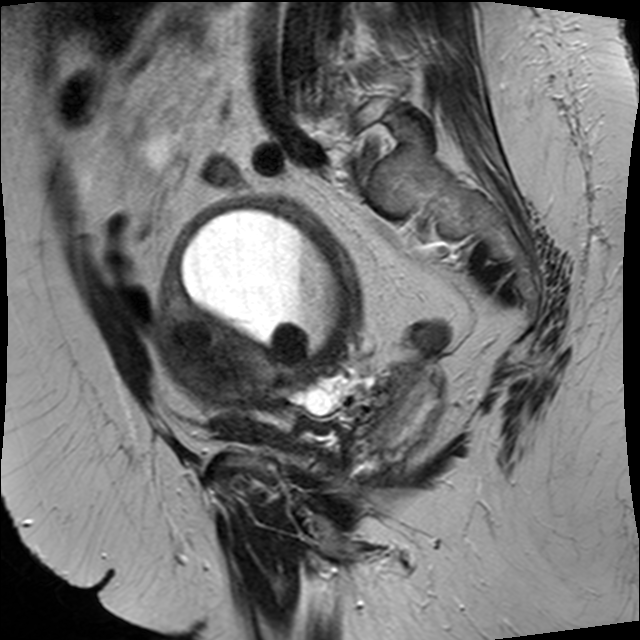
Pelvic MRI for cervical cancer, one sagittal slice; position 23 of 34 along the scan axis; T2-weighted; 1.5 T; TE 89 ms, TR 3320 ms; 4 mm slice thickness; 640 × 640 image matrix, field of view 260 × 260 mm. Patient: female, 50 years.
Structures marked on this image (manually delineated by an expert):
- uterus and cervix: bounding box [x1, y1, x2, y2] px = [156, 195, 437, 446]